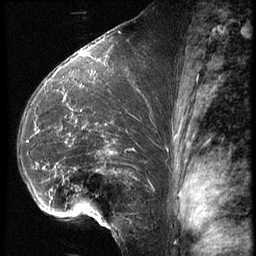
Breast MRI (dynamic contrast-enhanced), one sagittal slice; position 36 of 62 along the scan axis; 3 images stored at this slice position (order not interpretable as contrast timing); 1.5 T; TE 4.2 ms, TR 9 ms; 2.5 mm slice thickness; 256 × 256 image matrix. Patient: female, 39 years. From the clinical record (not read from this slice): setting: breast cancer imaged before/during neoadjuvant chemotherapy; receptor status: HER2-positive.
Annotated regions visible in this slice (semi-automatically segmented with operator editing):
- analysis volume of interest (the breast-tissue region the enhancement analysis was run in; not a lesion): bounding box (x1, y1, x2, y2) in pixels: (18, 64, 160, 228)
- tumour enhancement mask (voxels above the 140 % enhancement threshold inside the analysis volume of interest): (33, 110, 128, 215)